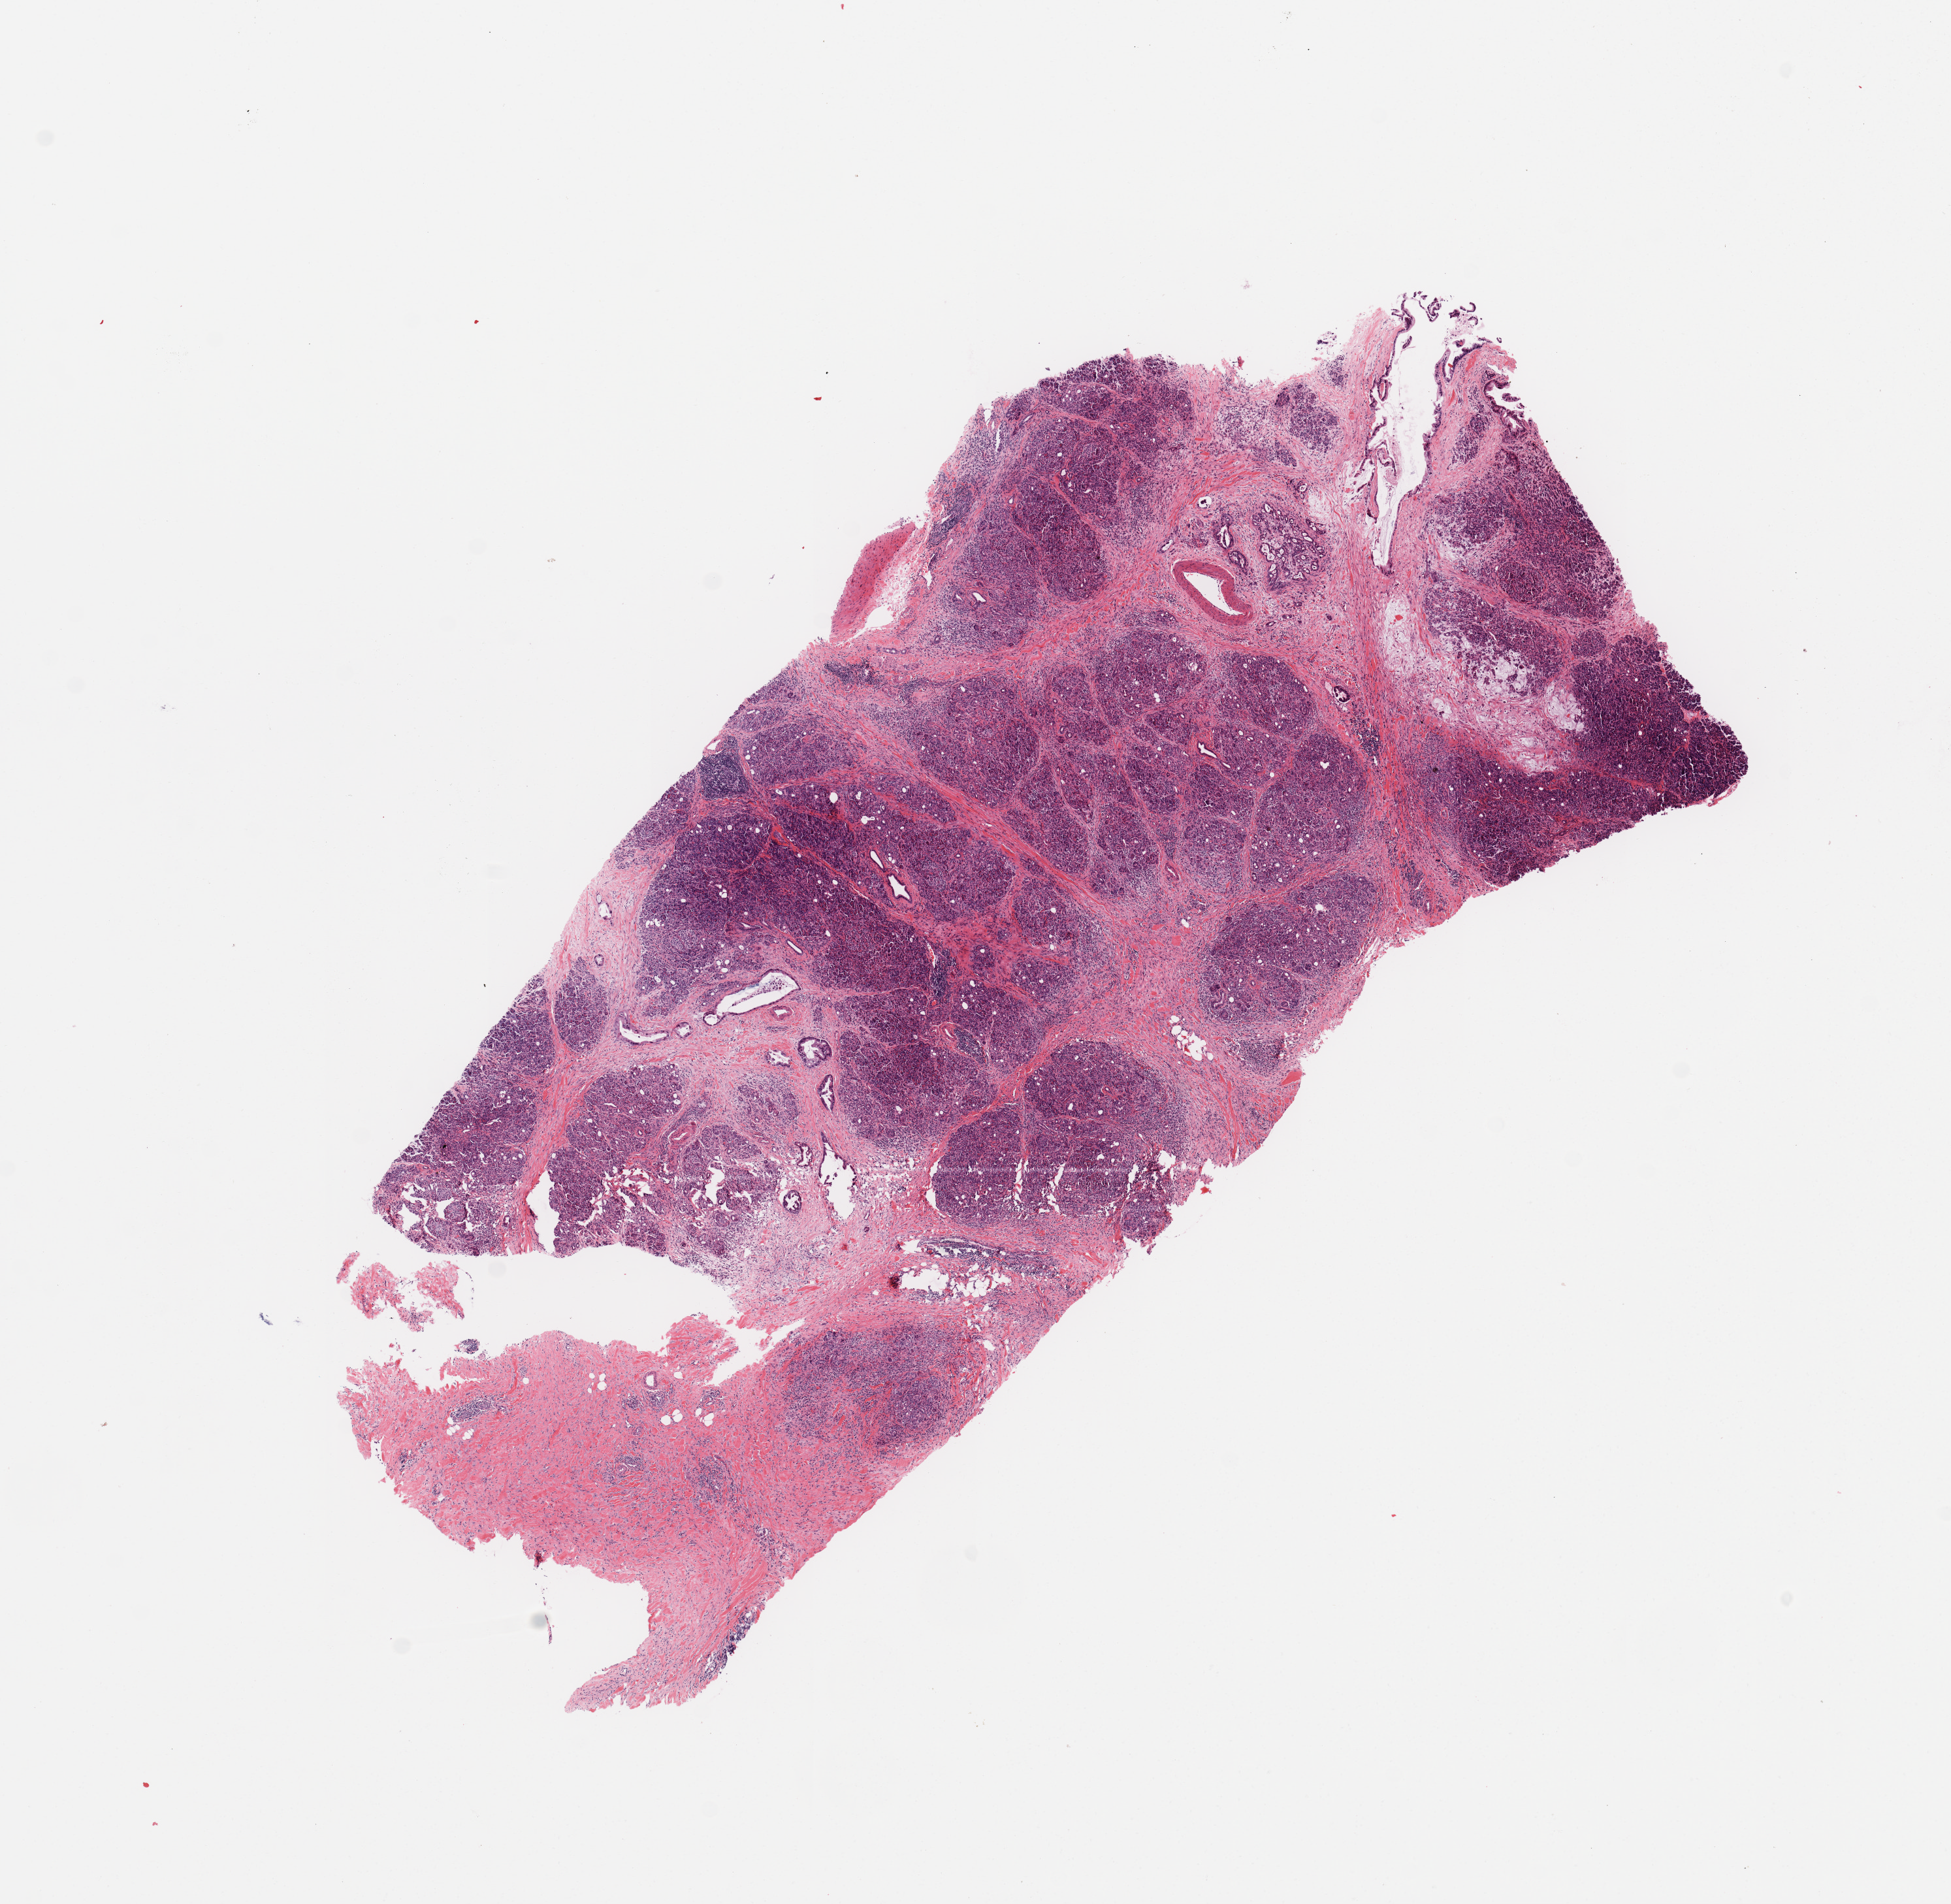
Digitized Hematoxylin and eosin (H&E) stained tissue section (whole slide) — shown as a low-resolution overview of the whole scanned area (about 11.8 x 11.5 mm, acquisition: 20x scan). Tumour tissue sample, sampled site: pancreas. Patient: male, age 31 years. Histologic grade: G1 (well differentiated). Slide review estimates, as recorded: tumour nuclei 10%, necrosis 0%.
Primary tumour site (as recorded): body. AJCC pathologic stage: IIB. Diagnosis: Infiltrating duct carcinoma, NOS.